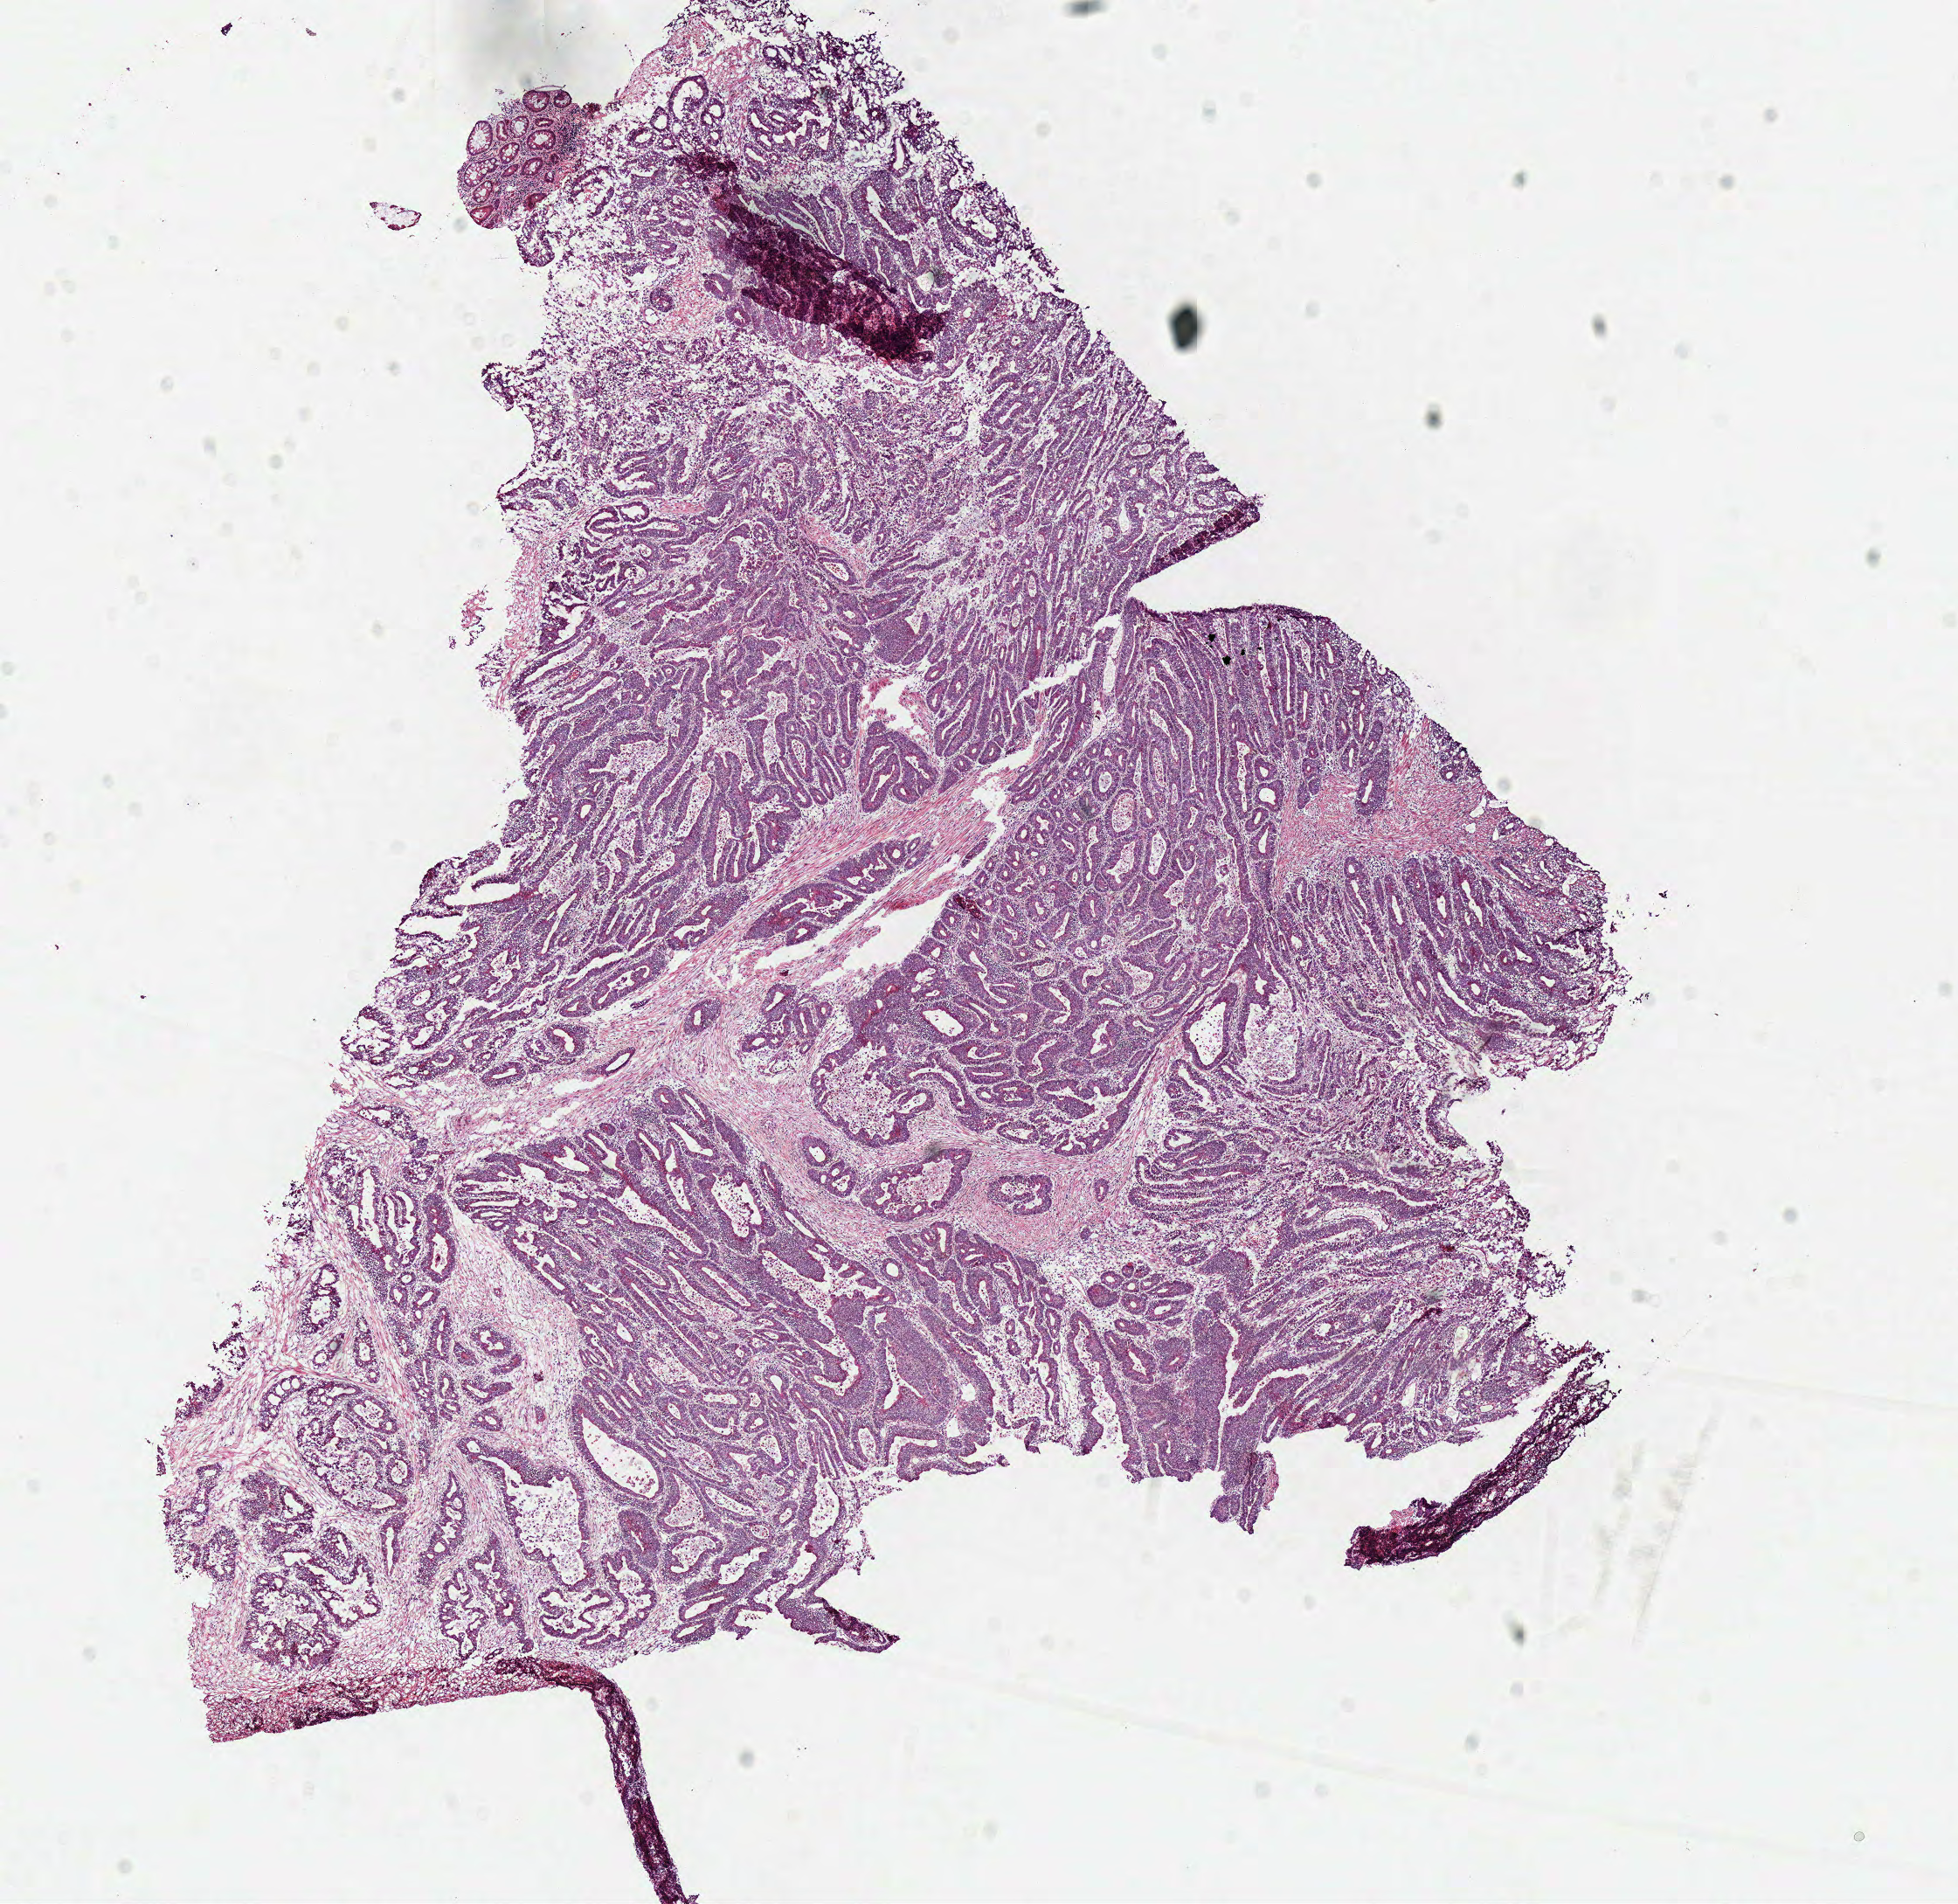
Digitized H&E tissue section (whole slide) — shown as a low-resolution overview of the whole scanned area (about 8.8 x 8.6 mm), frozen section, colon, primary tumour sample. Male patient; age at initial diagnosis 75 years. Slide review estimates, as recorded: tumour cells 78%, tumour nuclei 80%, normal cells 2%, stromal cells 15%, necrosis 5%.
Diagnosis: Adenocarcinoma, NOS (cecum). AJCC pathologic stage: IV. Lymph nodes positive (case pathology): 2 of 10 examined.